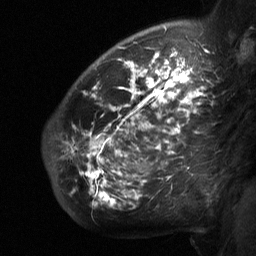
Breast MRI (dynamic contrast-enhanced), one sagittal slice; slice 48 of 64 in the series (ordered by position); dynamic contrast-enhanced study with each time point stored as its own series, time point 2 of 3 at this slice position (early post-contrast, ordered by acquisition time); 1.5 T; TE 4.8 ms, TR 27 ms; 2 mm slice thickness; 256 × 256 image matrix, field of view 200 × 200 mm. Patient: female, 50 years. Case-level facts recorded for this patient, not image findings: setting: breast cancer imaged before/during neoadjuvant chemotherapy; receptor status: HER2-positive.
Annotated regions visible in this slice (semi-automatically segmented with operator editing):
- analysis volume of interest (the breast-tissue region the enhancement analysis was run in; not a lesion): box from (x=49, y=62) to (x=215, y=213) px
- tumour enhancement mask (voxels above the 90 % enhancement threshold inside the analysis volume of interest): (x=72, y=62)–(x=204, y=205)